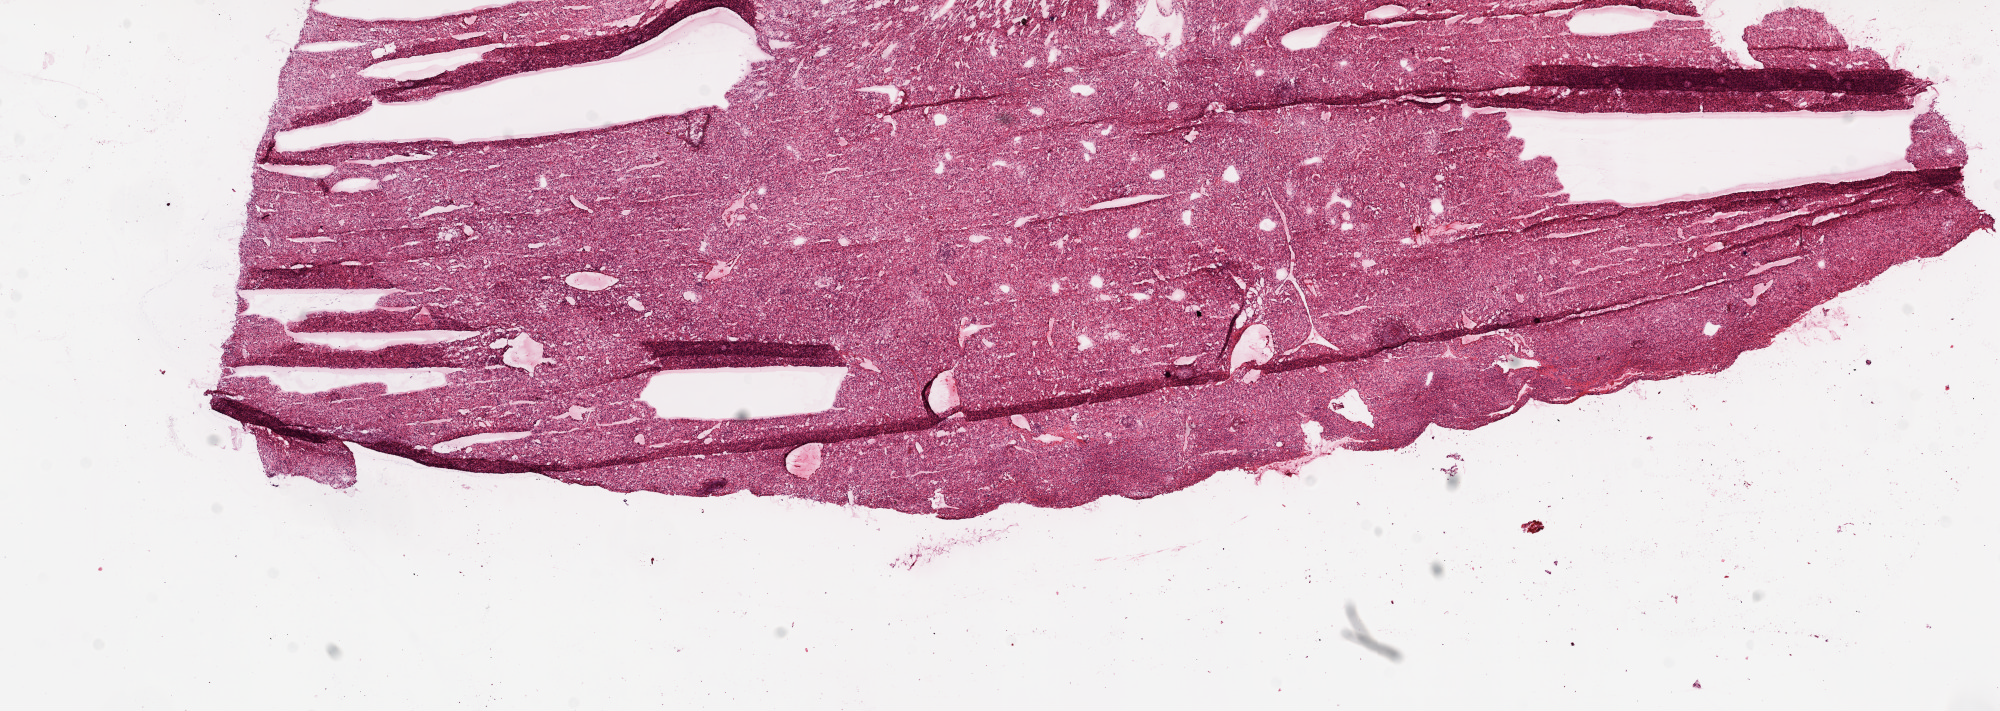
Hematoxylin and eosin (H&E) stained whole-slide image — low-resolution overview of the scanned area, about 16.0 x 5.7 mm; frozen section from the top of the tissue portion; primary tumour sample from the kidney. Male patient; age at initial diagnosis 52 years. Histologic grade: G2 (moderately differentiated). Composition of this section per pathologist review: tumour cells 95%, tumour nuclei 90%, normal cells 0%, stromal cells 5%, necrosis 0%.
Pathologic diagnosis: Clear cell adenocarcinoma, NOS. TNM: T3a N0 M1. AJCC pathologic stage: IV. Laterality: right.